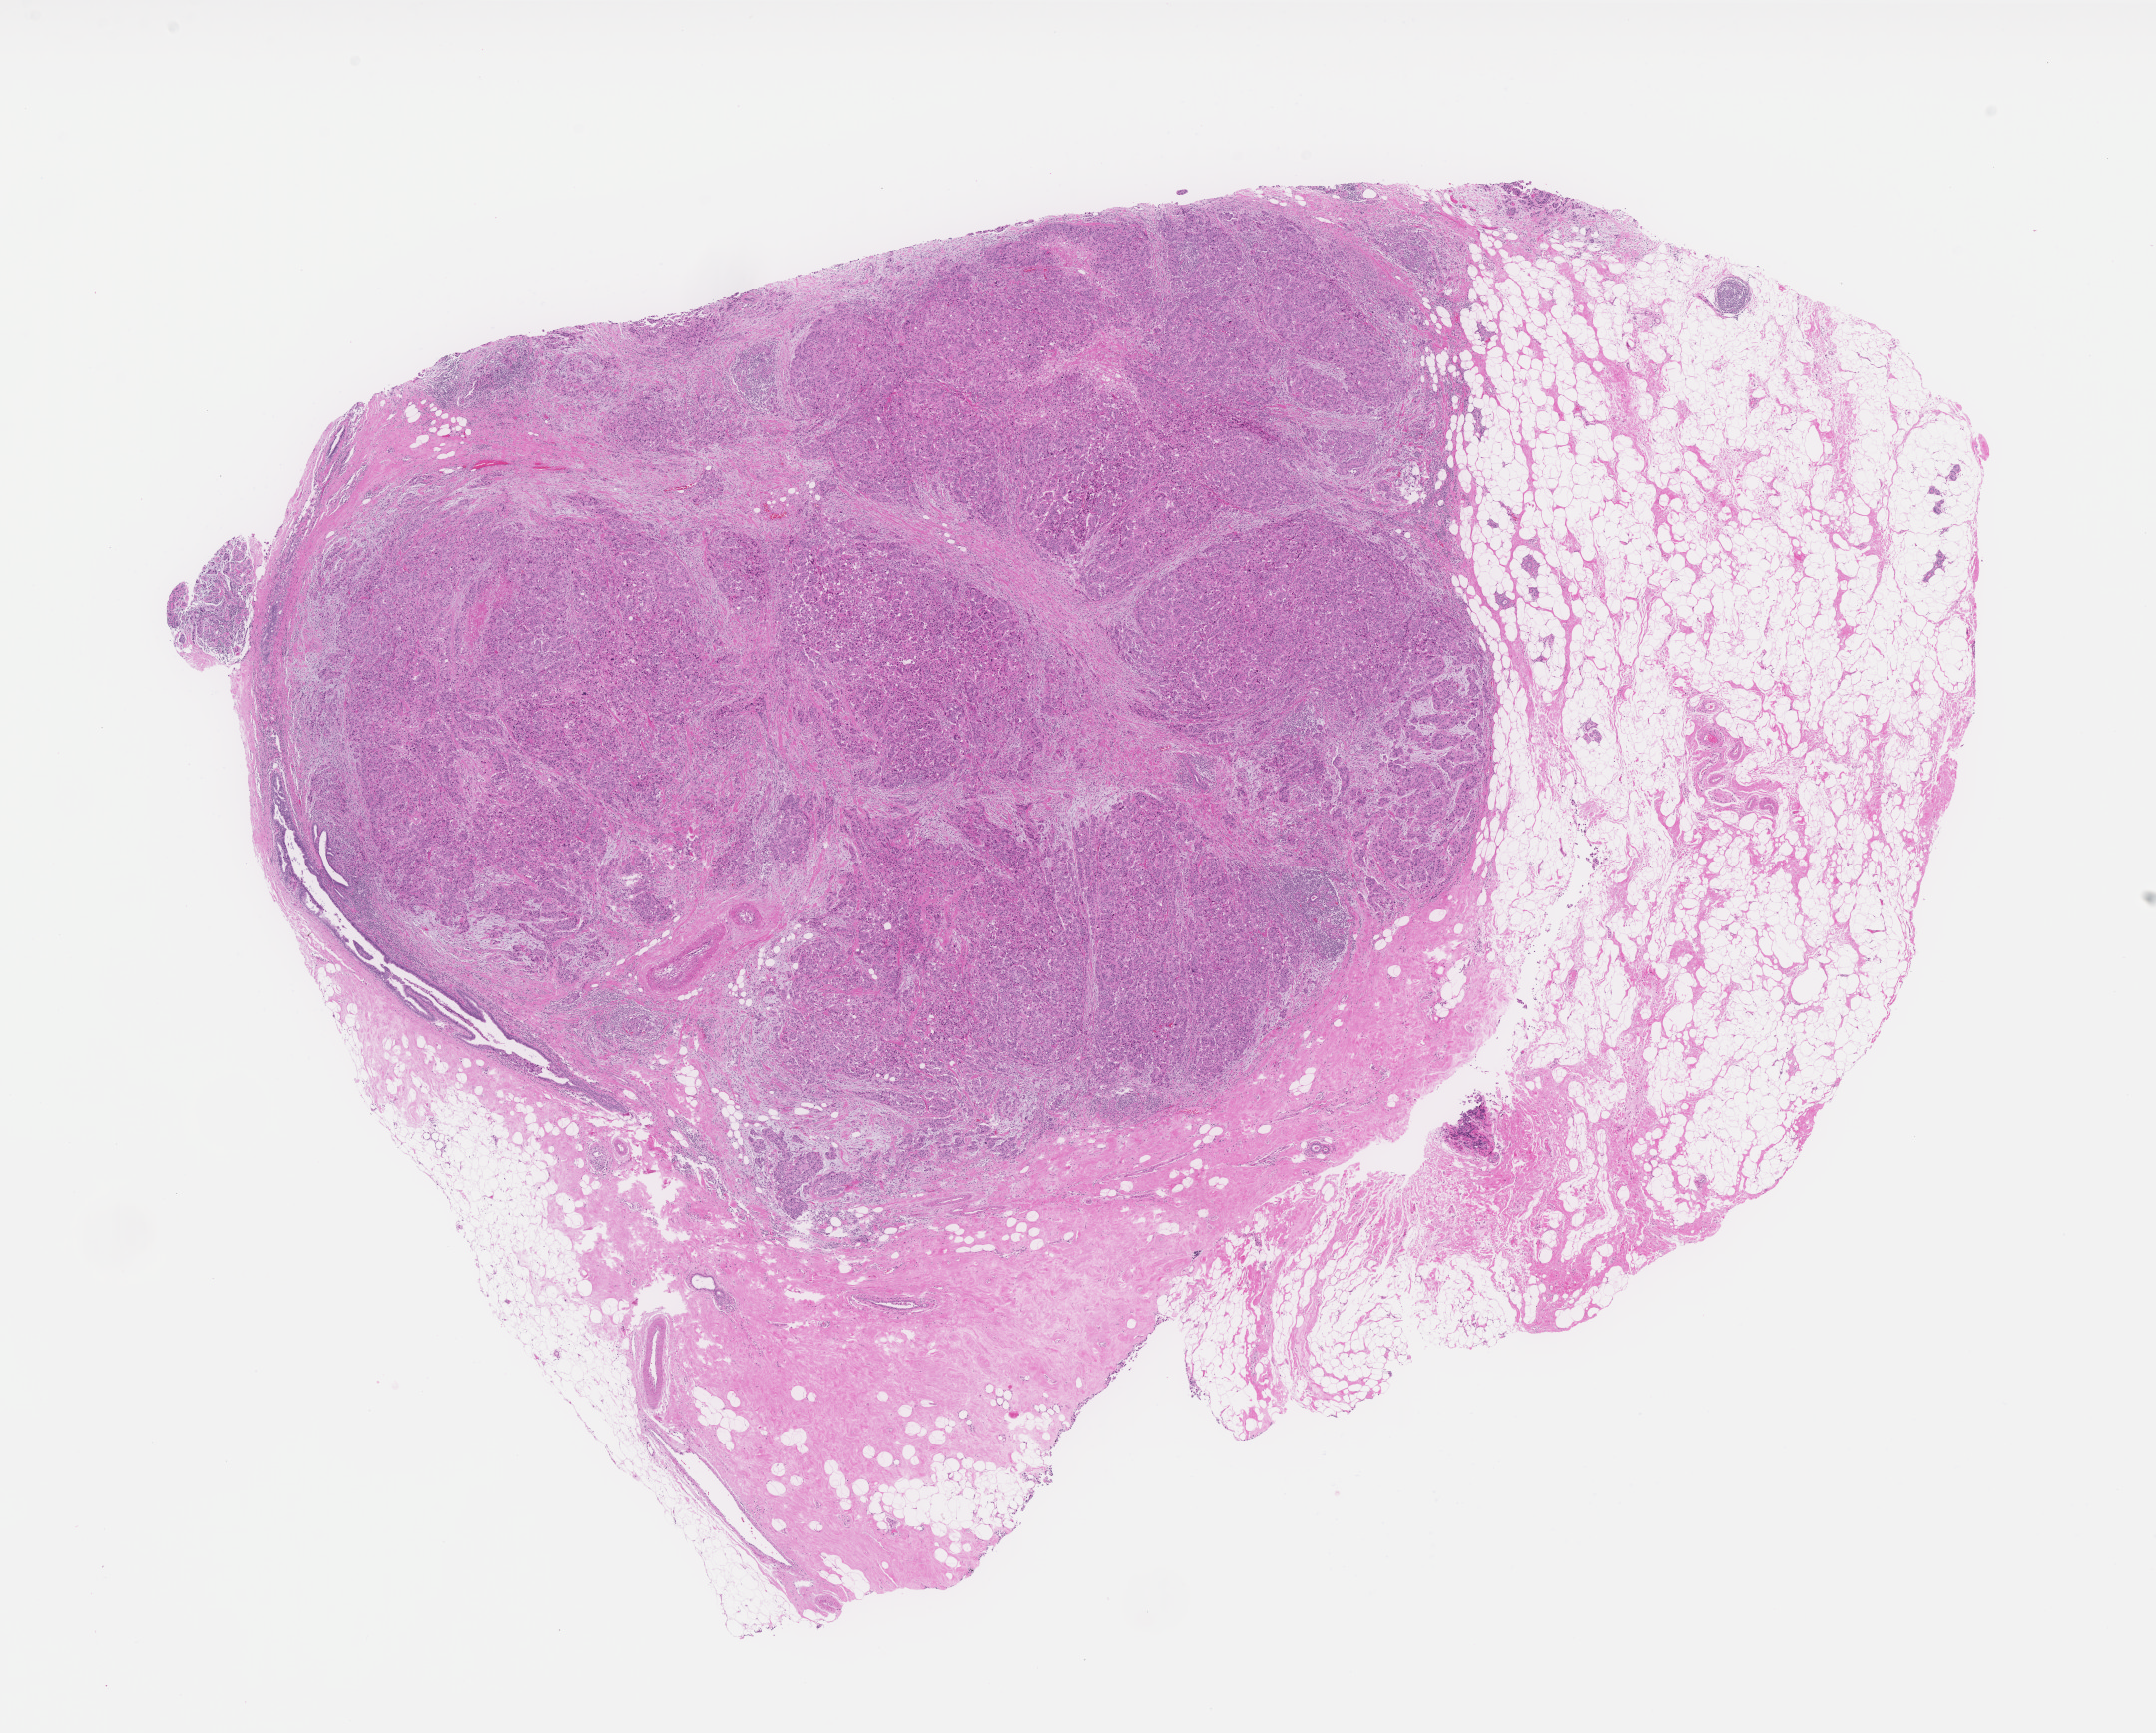
Whole-slide histology image, H&E-stained — a low-resolution overview of the entire scanned area, about 17.3 x 13.9 mm (from a 40x scan), formalin-fixed paraffin-embedded (FFPE) diagnostic section, breast, primary tumour sample. Patient: female, age at initial diagnosis 53 years.
* AJCC pathologic stage: IIIA
* laterality: left
* pathologic diagnosis: Infiltrating duct carcinoma, NOS